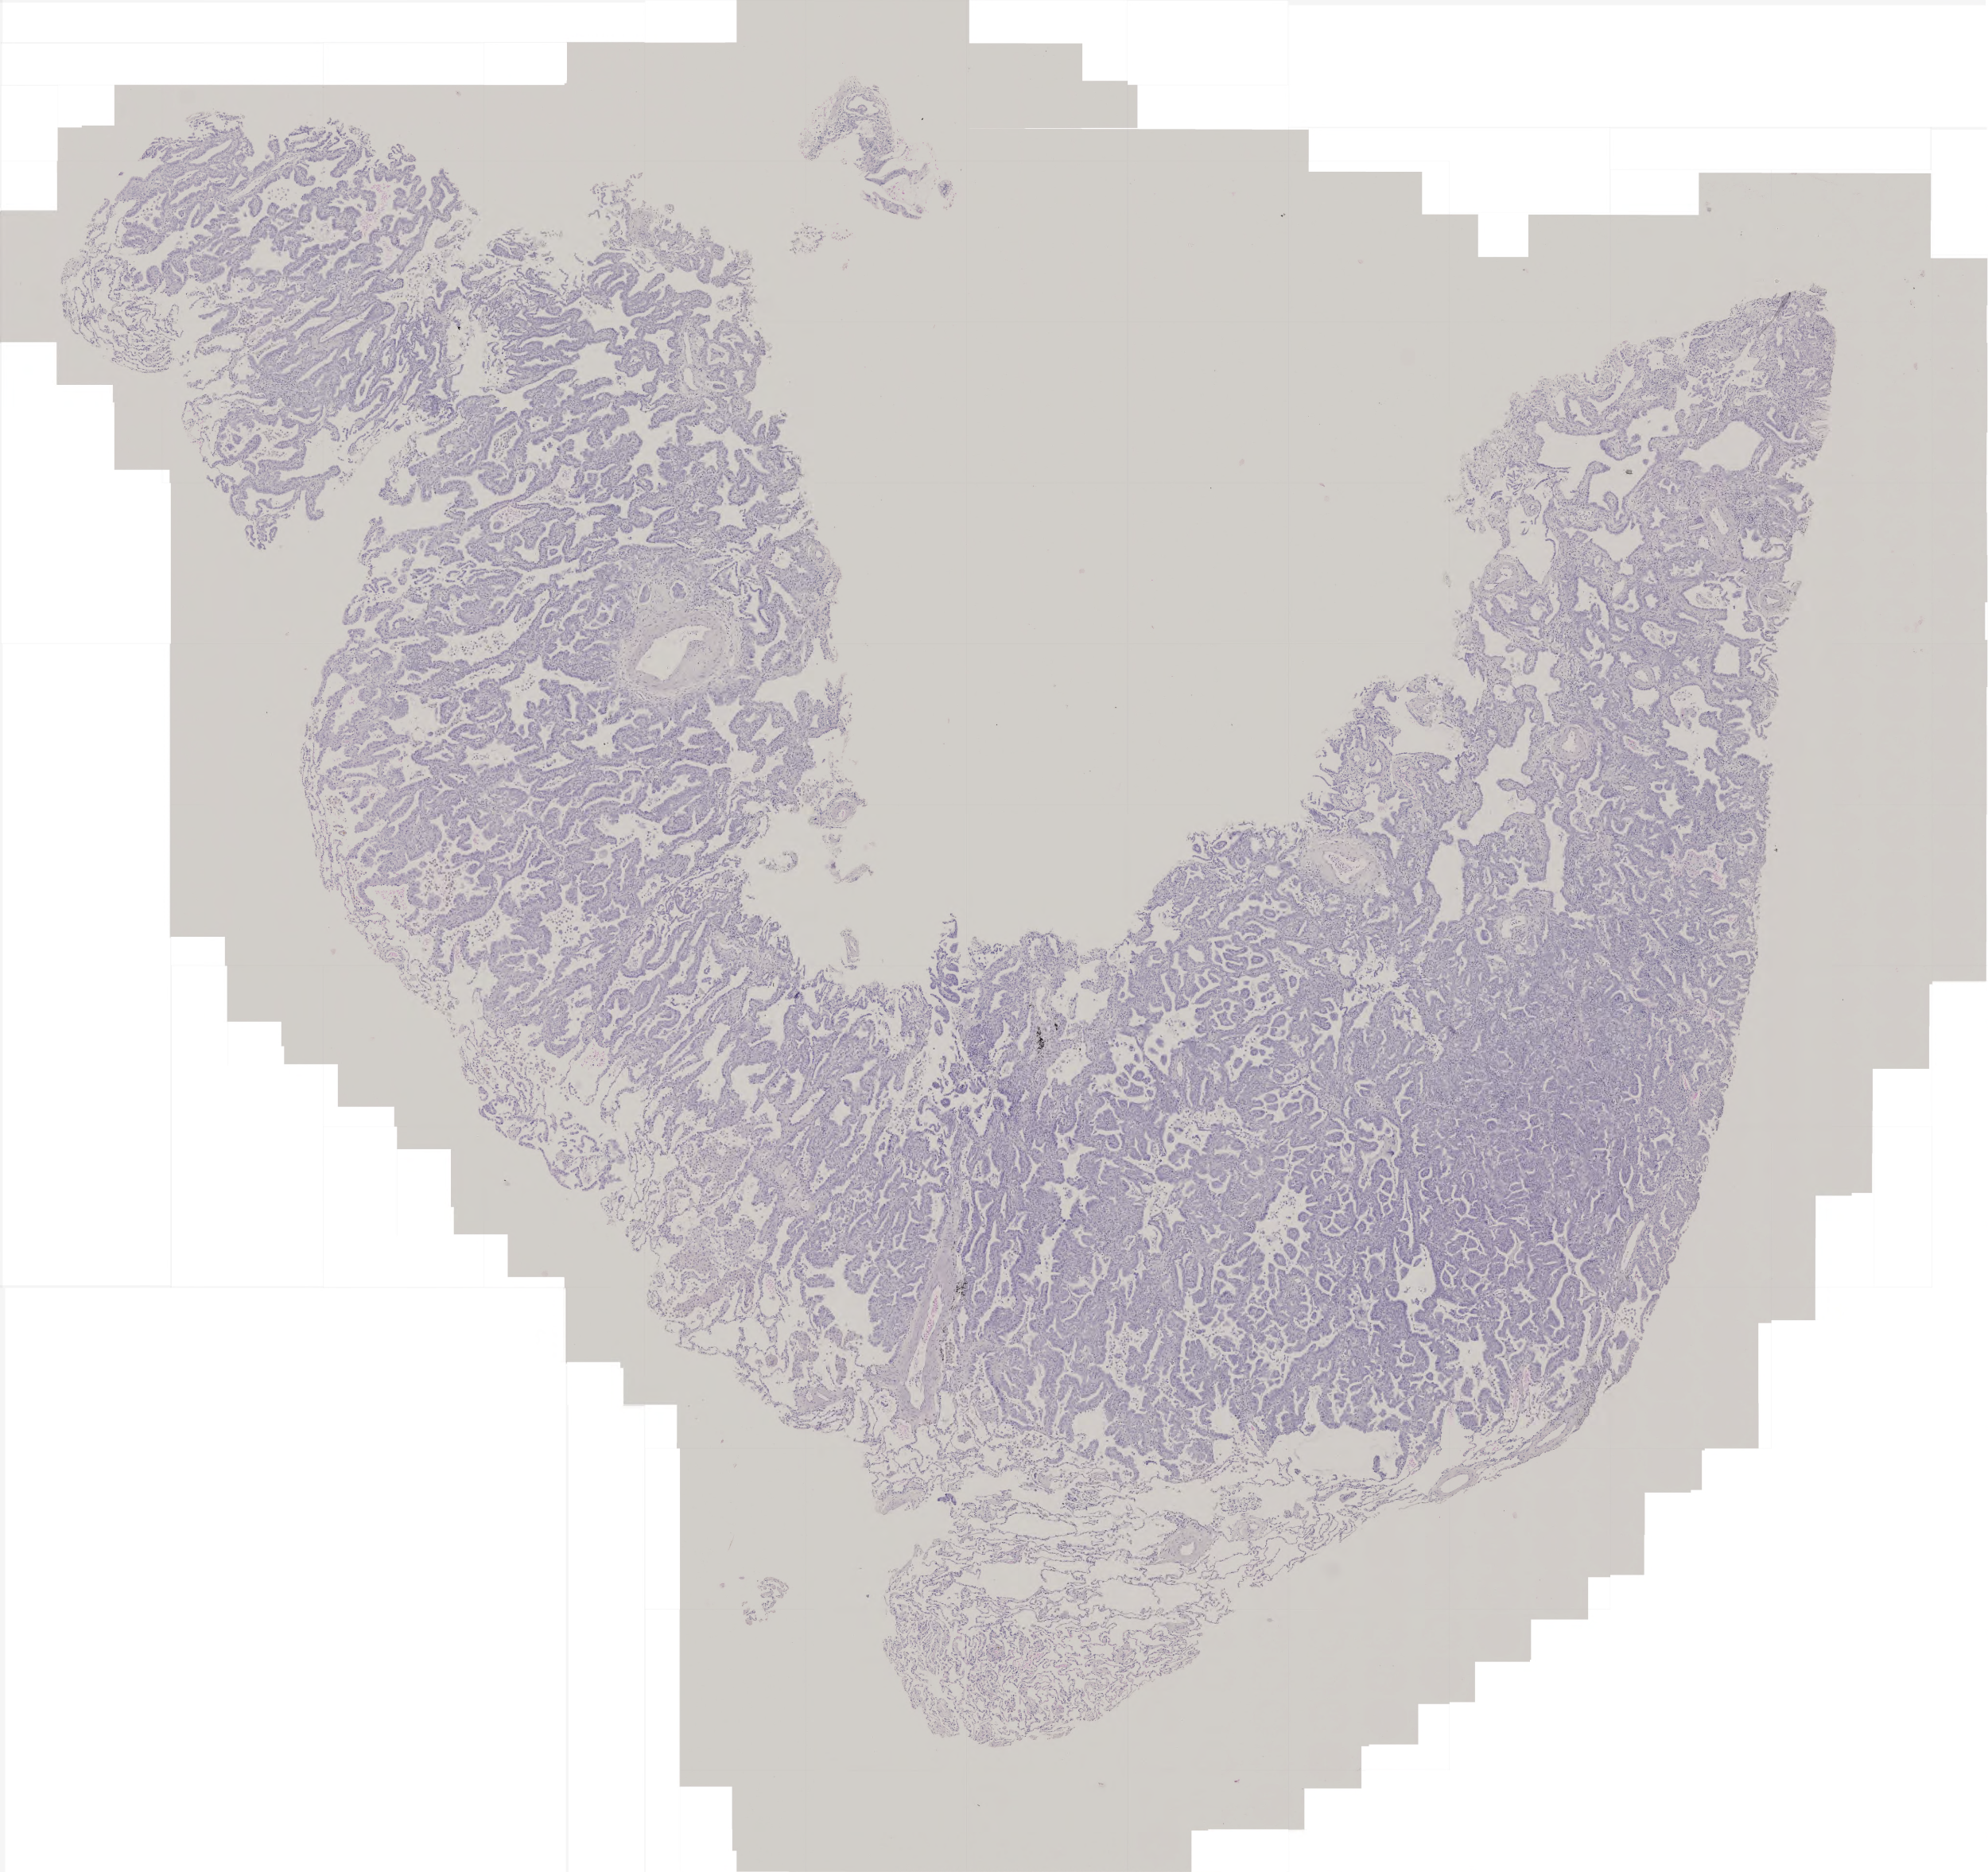
H&E whole-slide image, whole scanned area (about 5.0 x 4.7 mm) shown as a low-resolution overview; formalin-fixed paraffin-embedded (FFPE) diagnostic section; sample: primary tumour, lung. Patient: male, age at initial diagnosis 66 years.
Histologic diagnosis: Adenocarcinoma with mixed subtypes (lower lobe, lung). AJCC pathologic stage: IIIA (6th edition).